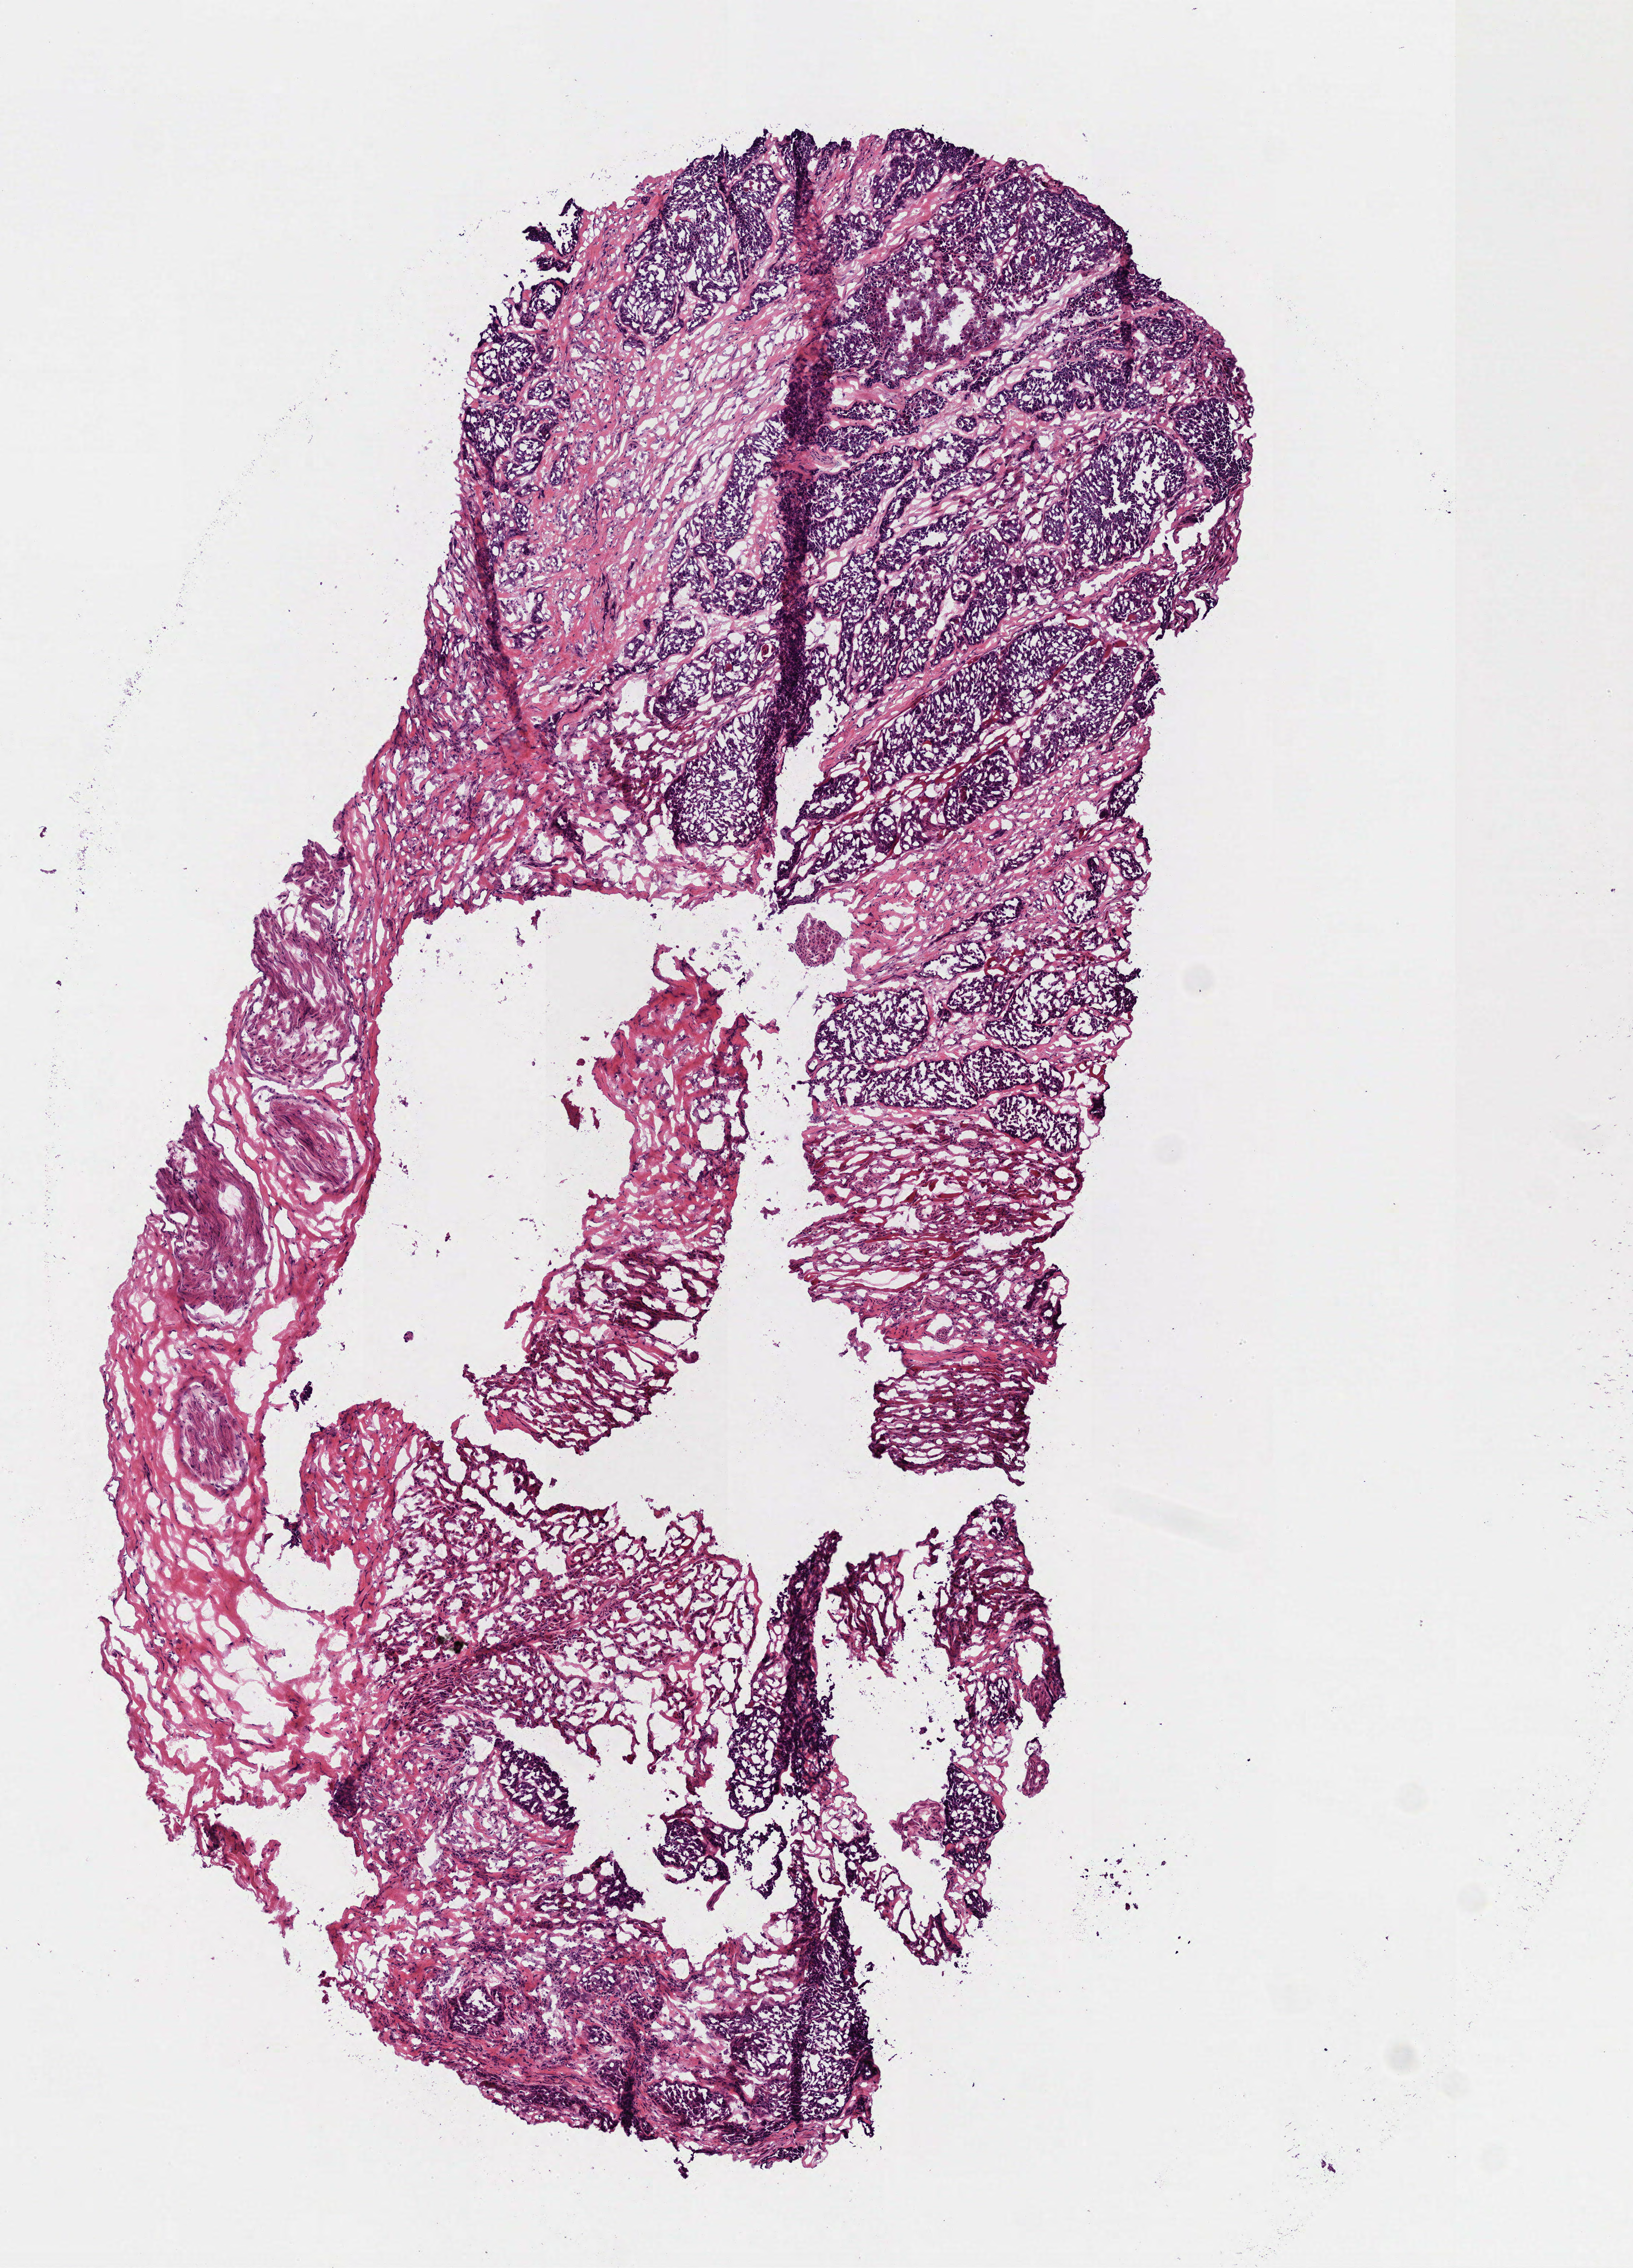
Whole-slide histology image, Hematoxylin and eosin (H&E) stained, low-resolution overview of the scanned area, about 4.5 x 6.3 mm (acquisition: 40x scan). Frozen section from the top of the tissue portion. Primary tumour sample from the head and neck. Male, age 60 years at initial diagnosis.
Diagnosis: Squamous cell carcinoma, NOS.